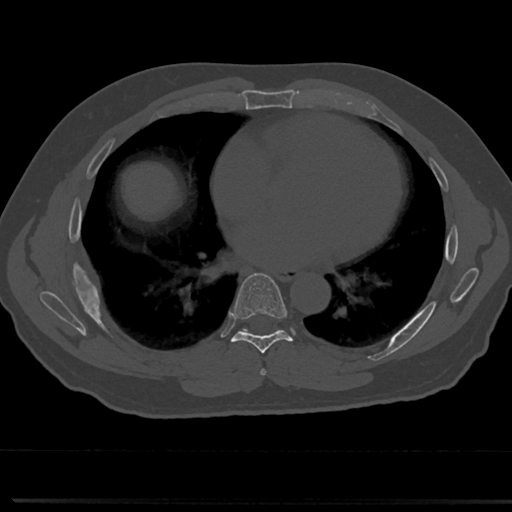
CT including the spine, one axial slice; reconstruction kernel Br40s/3; 120 kVp; bone window (W 1800 / L 400 HU); 0.5 mm slice thickness; 512 × 512 image matrix, field of view 355 × 355 mm. Male patient, age 61 years. From the clinical record (not read from this slice): primary cancer: prostate.
Annotated regions visible in this slice (semi-automatically segmented with operator editing):
- T6 vertebra: bounding box [x1, y1, x2, y2] px = [261, 340, 319, 376]
- T7 vertebra: [214, 275, 310, 358]